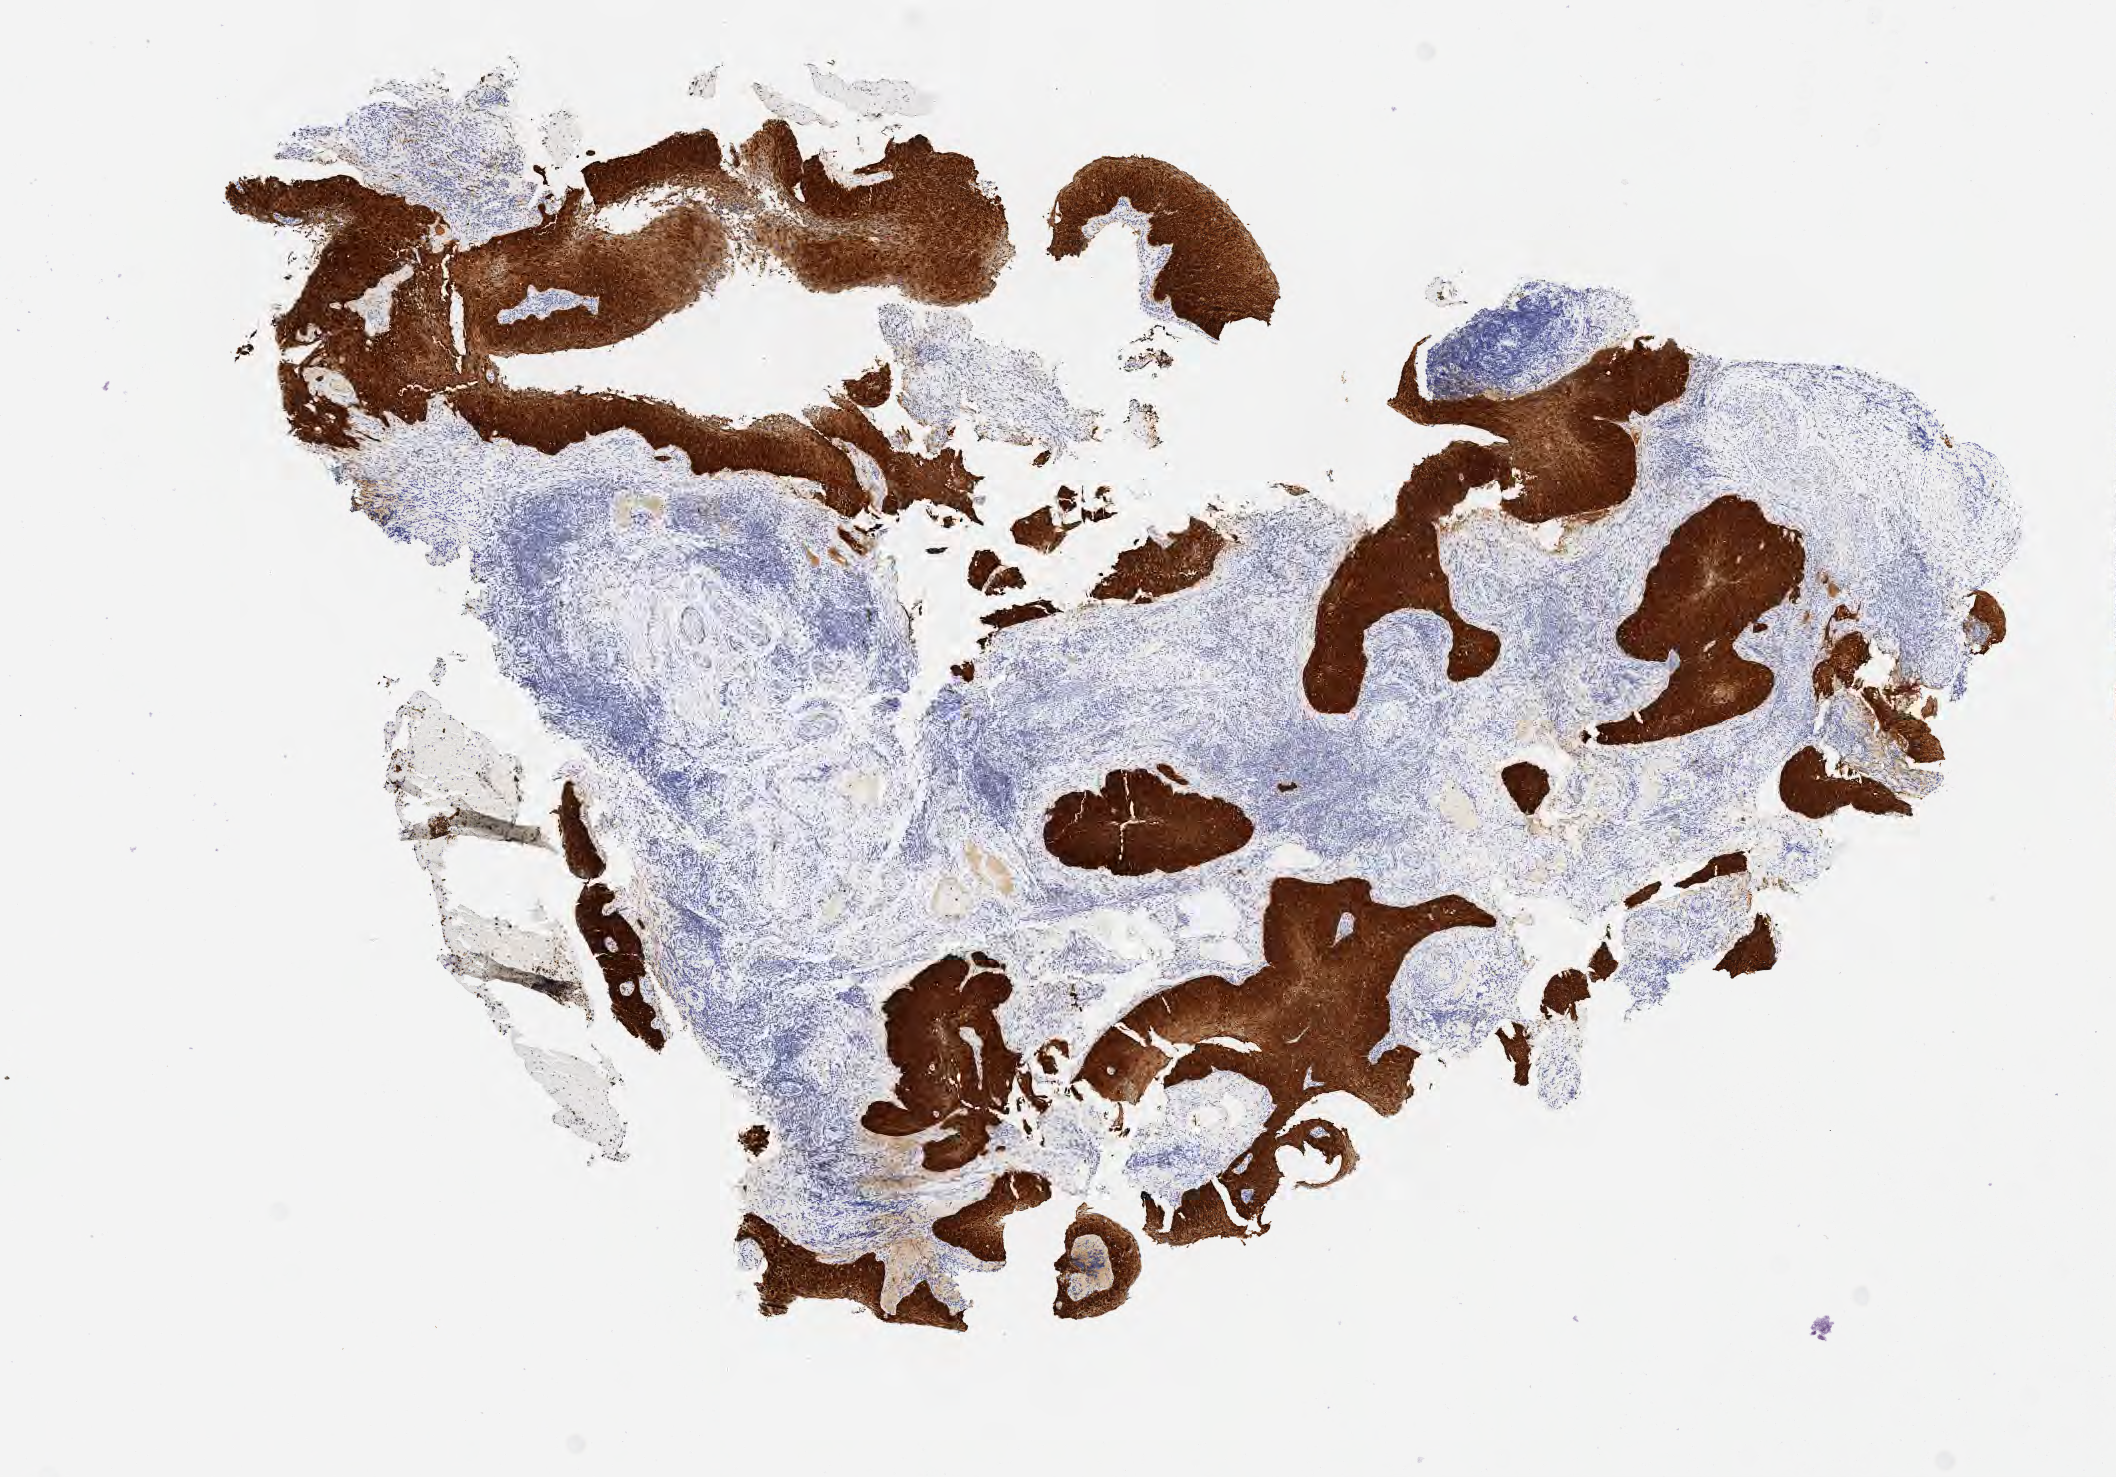
Whole-slide image, immunohistochemical stain for p16 (p16INK4a) — whole scanned area (about 8.6 x 6.0 mm) shown as a low-resolution overview, tumor tissue, anatomic site: cervix. Female patient, 50 years old.
Diagnosis: Squamous cell carcinoma, large cell, nonkeratinizing, NOS.